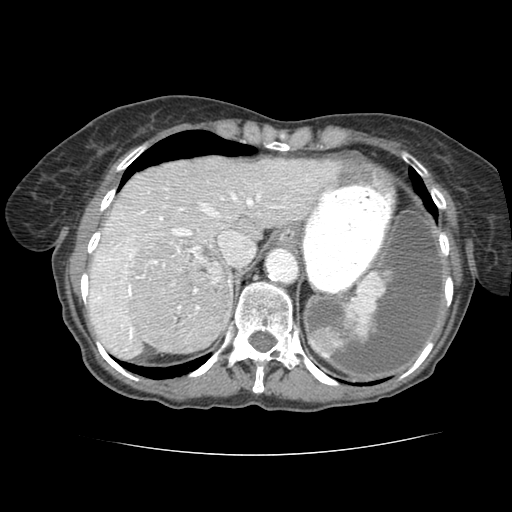
Contrast-enhanced abdominal CT (liver protocol), one axial slice. Slice 62 of 77 in the series (ordered by position). Reconstruction kernel STANDARD. 120 kVp. Soft-tissue window (W 400 / L 40 HU). 2.5 mm slice thickness. 512 × 512 image matrix, field of view 340 × 340 mm. Case-level facts recorded for this patient, not image findings: diagnosis: hepatocellular carcinoma (patient treated with transarterial chemoembolisation; whether this scan precedes or follows treatment is not stated here); TNM stage (as recorded): Stage-I; Child-Pugh class: A; tumour nodularity: uninodular.
Annotated regions visible in this slice (semi-automatic segmentation, software-assisted and operator-edited):
- liver parenchyma outside the tumour (the mass and vessels are separate outlines, so this box may not span the whole liver): bounding box <84,154,332,354> (left, top, right, bottom; pixels)
- mass: <126,239,229,347>
- liver vessels: <91,180,280,310>